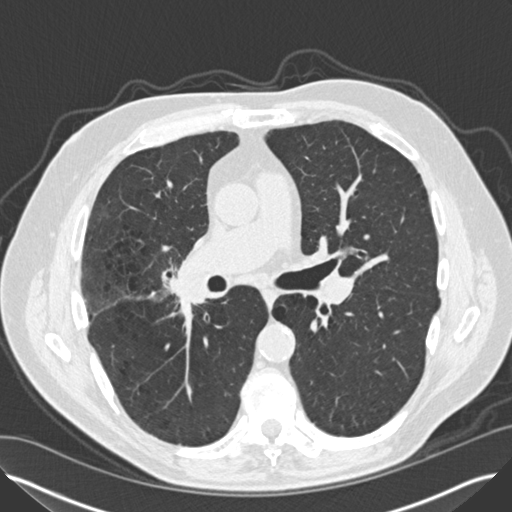
Axial slice from a low-dose chest CT screening exam; second screening round (one year after baseline); lung window (W 1500 / L -600 HU); slice 70 of 149 in the series; 512 × 512 image matrix. Male, age 65 years at enrolment. Current smoker at enrolment.
Lesion marked by an expert reader, bounding box (x1, y1, x2, y2) in pixels: (151, 263, 210, 315). Screening reader's record for this exam (one nodule recorded; not confirmed to be the boxed lesion): non-calcified nodule or mass ≥4 mm, left lower lobe, 12 × 8 mm, smooth margins, soft tissue attenuation, pre-existing on the prior screen: yes; interval growth: yes. Note: the box lies in the patient's right hemithorax on this image, whereas the reader's record names the left lung; they may be different findings. Later outcome: lung cancer diagnosed 67 days after this screen — non-small cell carcinoma, left lower lobe, right hilum, poorly differentiated (G3), stage IV (AJCC 6th edition), 5 mm at pathology.